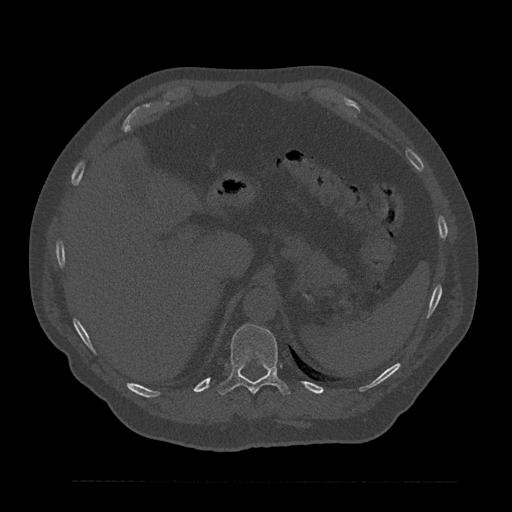
CT including the spine, one axial slice; position 296 of 797 along the scan axis; reconstruction kernel Br40s/3; 120 kVp; bone window (W 1800 / L 400 HU); 0.5 mm slice thickness; 512 × 512 image matrix. Male patient, age 61 years. From the clinical record (not read from this slice): primary cancer: prostate.
Annotated regions visible in this slice (semi-automatically segmented with operator editing):
- T11 vertebra: box from (x=217, y=324) to (x=290, y=395) px